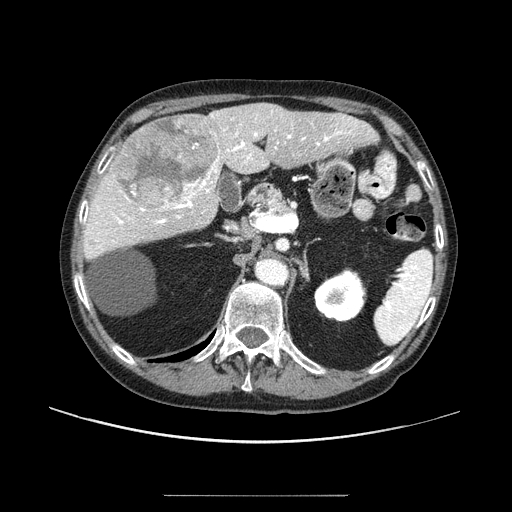
Contrast-enhanced abdominal CT (liver protocol), one axial slice; slice 51 of 91 in the series (ordered by position); reconstruction kernel STANDARD; 100 kVp; one of 2 acquisitions stored at this slice position; soft-tissue window (W 400 / L 40 HU); 2.5 mm slice thickness; 512 × 512 image matrix. Case-level facts recorded for this patient, not image findings: diagnosis: hepatocellular carcinoma (patient treated with transarterial chemoembolisation; whether this scan precedes or follows treatment is not stated here); TNM stage (as recorded): Stage-I; Child-Pugh class: A; tumour differentiation: moderately differentiated.
Structures marked on this image (semi-automatically segmented with operator editing):
- liver parenchyma outside the tumour (the mass and vessels are separate outlines, so this box may not span the whole liver): bounding box [x1, y1, x2, y2] px = [84, 102, 376, 260]
- mass: [110, 113, 221, 209]
- liver vessels: [96, 119, 351, 248]